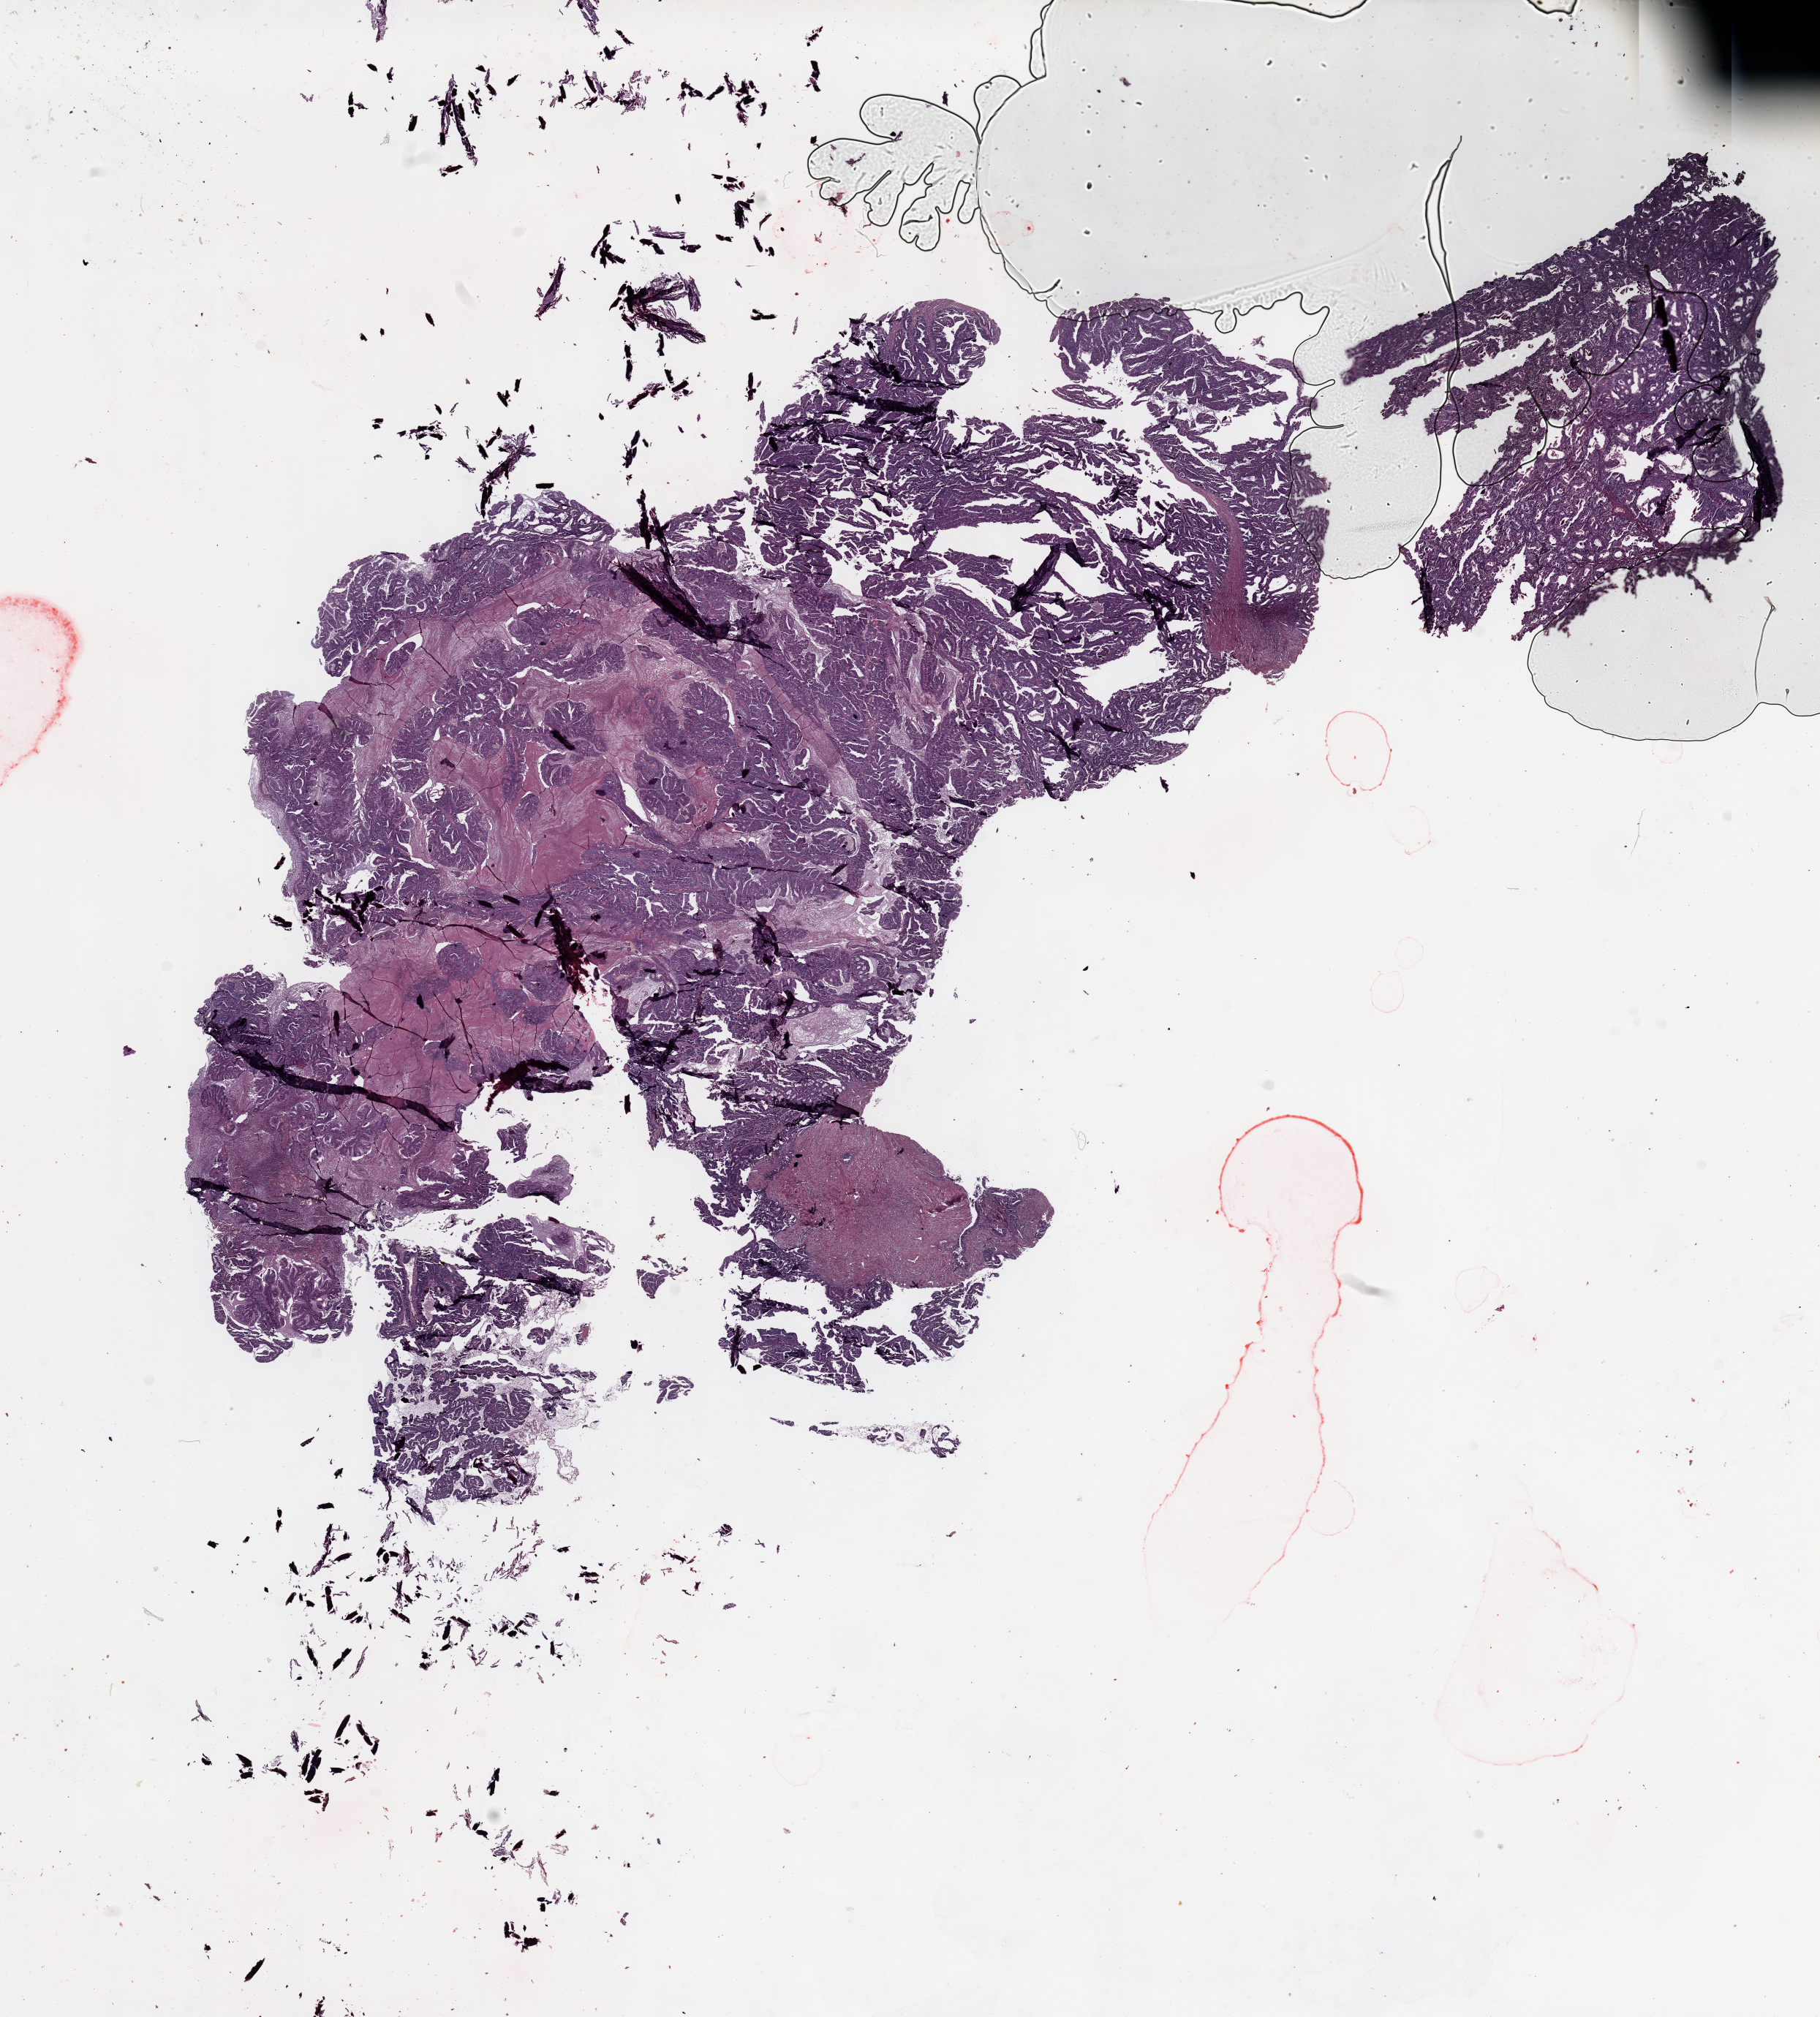
H&E whole-slide image, low-resolution overview of the scanned area, about 19.7 x 21.8 mm, tumour tissue sample, sampled site: uterus. Female, 70 y/o. Histologic grade: G2 (moderately differentiated). Pathologist review of this section (percent, as recorded): tumour nuclei 90%, necrosis 5%.
• histologic diagnosis: Endometrioid adenocarcinoma, NOS
• AJCC pathologic stage: I